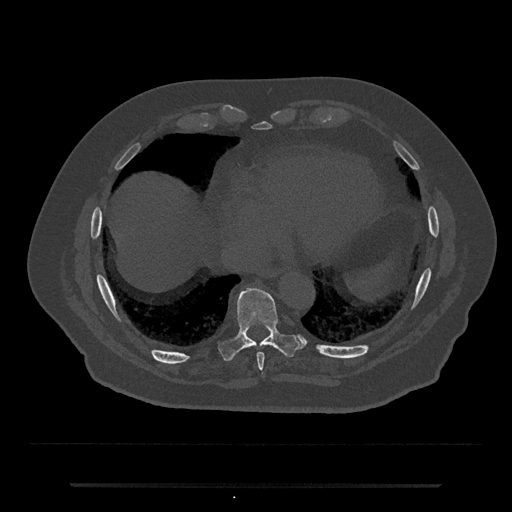
CT including the spine, one axial slice. Reconstruction kernel Br40s/3. Bone window (W 1800 / L 400 HU). 0.5 mm slice thickness. 512 × 512 image matrix, field of view 434 × 434 mm. Patient: male, 80 years. Case-level facts recorded for this patient, not image findings: primary cancer: prostate.
Structures marked on this image (semi-automatically segmented with operator editing):
- T8 vertebra: bounding box <257,353,264,375> (left, top, right, bottom; pixels)
- T9 vertebra: <219,286,303,361>